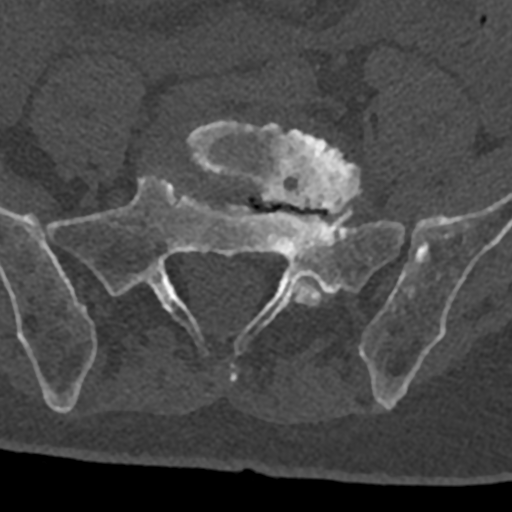
CT including the spine, one axial slice; position 164 of 797 along the scan axis; reconstruction kernel Br40s/3; bone window (W 1800 / L 400 HU); 512 × 512 image matrix, field of view 160 × 160 mm. Patient: male, 74 years. Case-level facts recorded for this patient, not image findings: primary cancer: renal; vertebrae with lytic lesions (as recorded): T10, L1, L2, L3, L4, L5.
Structures marked on this image (semi-automatically segmented with operator editing):
- L5 vertebra: bounding box <187,121,361,306> (left, top, right, bottom; pixels)